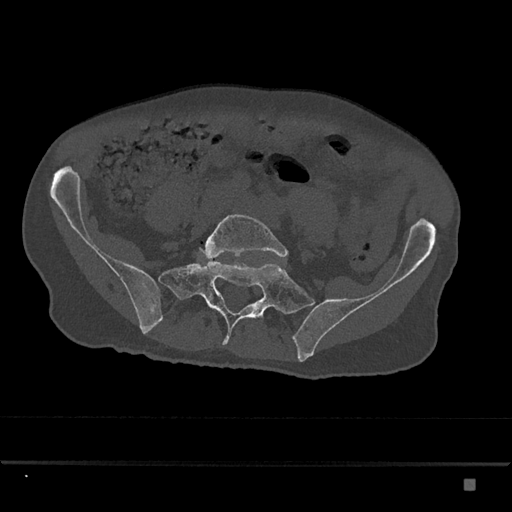
CT including the spine, one axial slice. Slice 240 of 797 in the series (ordered by position). Bone window (W 1800 / L 400 HU). 0.5 mm slice thickness. 512 × 512 image matrix, field of view 390 × 390 mm. Male patient, age 72 years. From the clinical record (not read from this slice): primary cancer: prostate.
Outlined on this slice (semi-automatically segmented with operator editing):
- L5 vertebra: bounding box (x1, y1, x2, y2) in pixels: (203, 214, 288, 260)